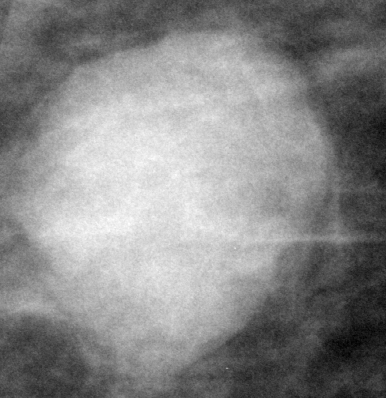
Cropped region of a digitized screen-film mammogram centred on a radiologist-marked abnormality; right breast; CC view; BI-RADS breast density category 2 (scale 1–4).
Mass, shape round, margins circumscribed; BI-RADS assessment category 4; pathology (as recorded): benign.